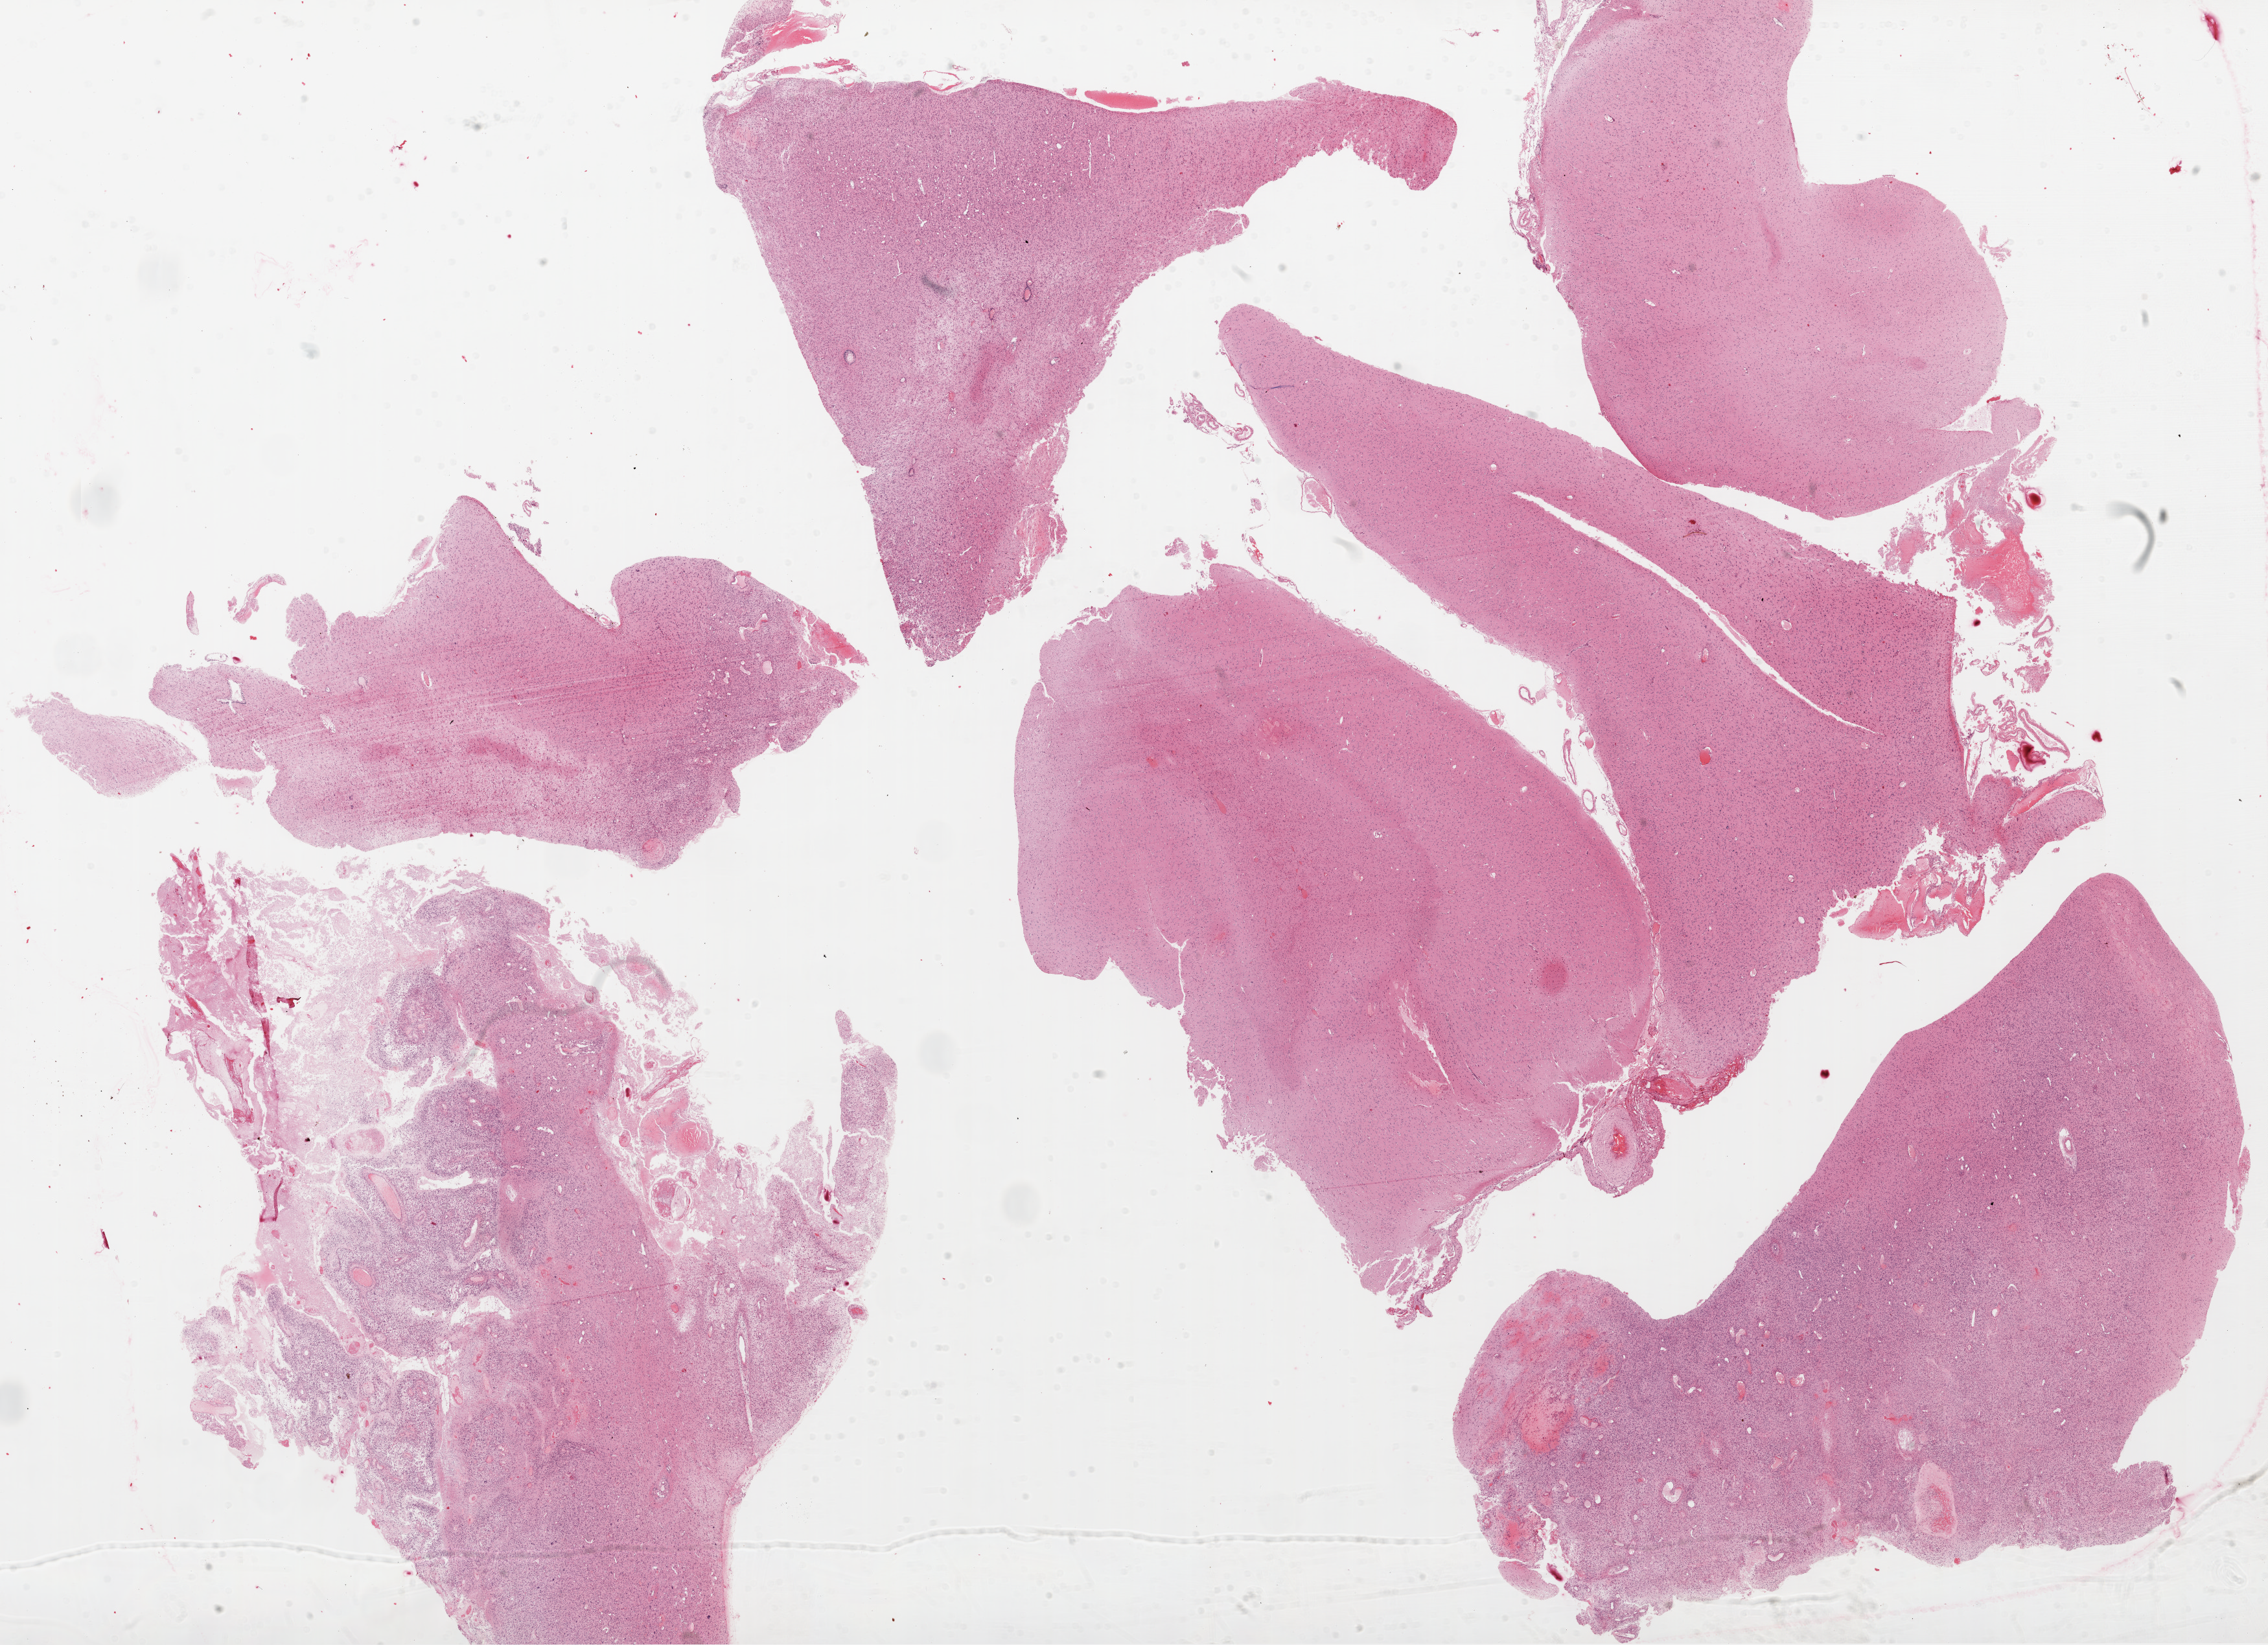
H&E-stained whole-slide image, a low-resolution overview of the entire scanned area, about 28.1 x 20.4 mm (acquisition: 20x scan), FFPE section, sample: primary tumour, brain. Female patient; age at initial diagnosis 33 years.
Pathologic diagnosis: Glioblastoma.